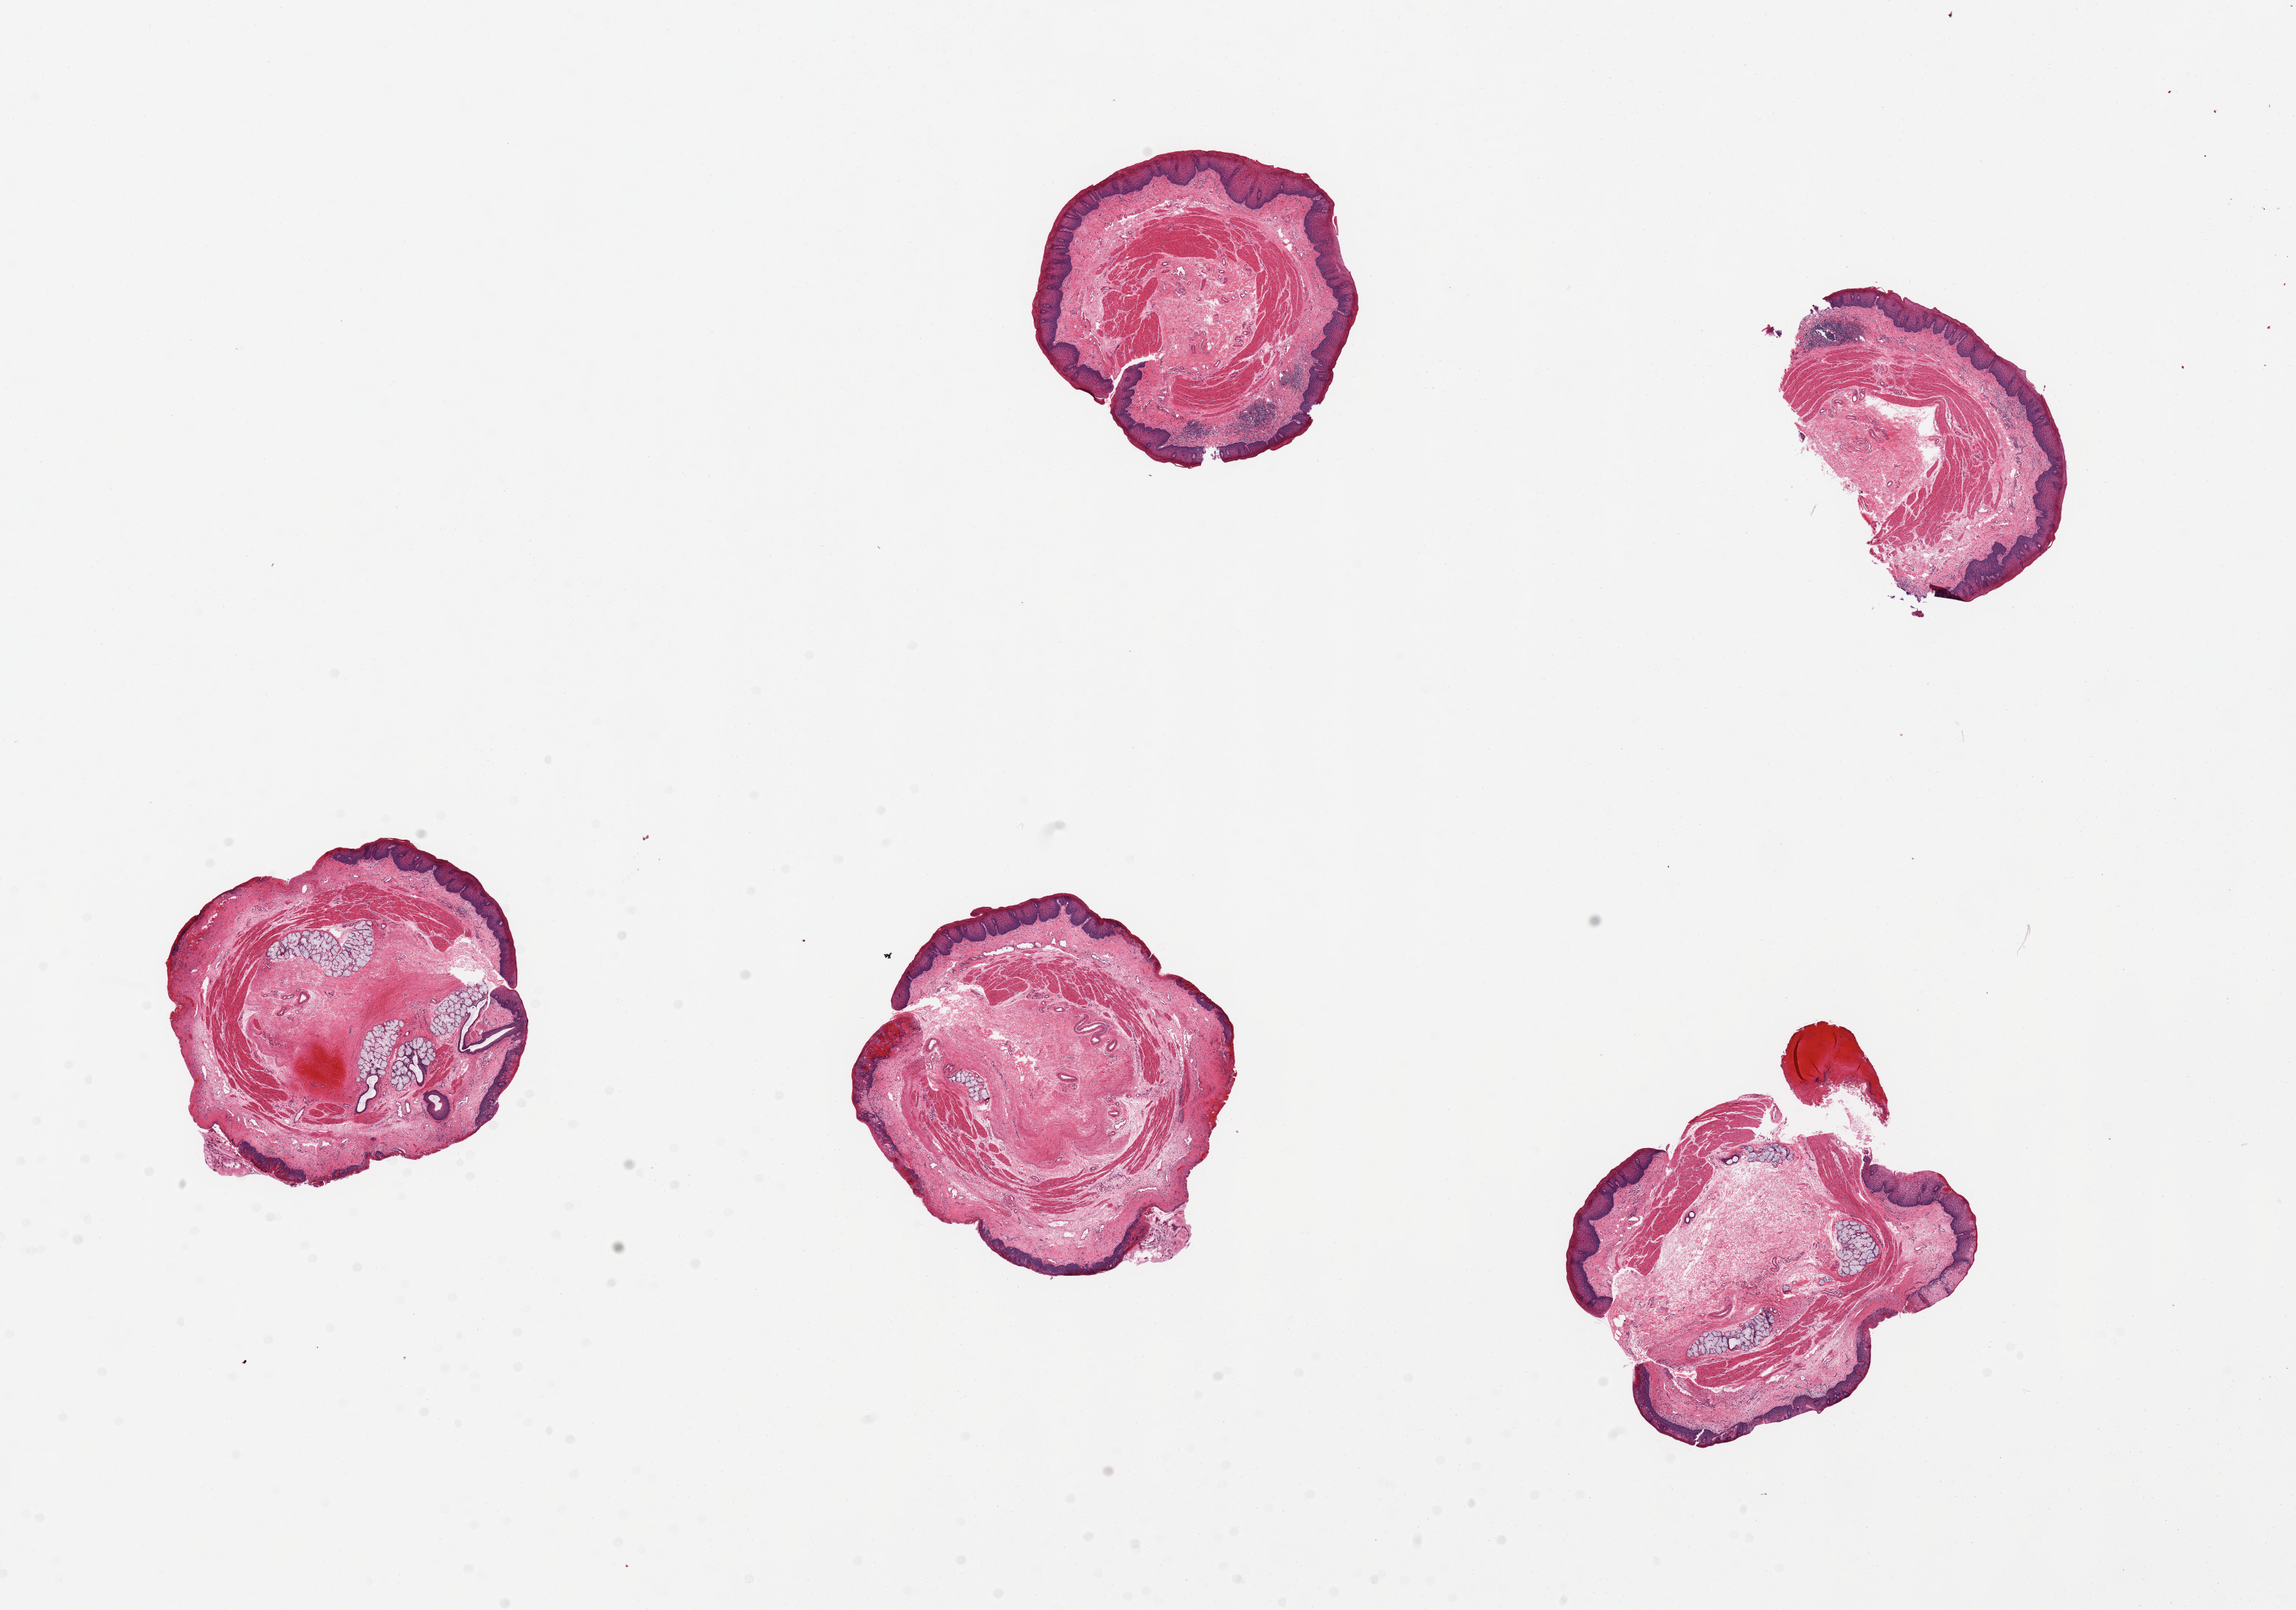
Digitized hematoxylin and eosin (H&E)-stained section, whole scanned area (about 24.6 x 17.3 mm) shown as a low-resolution overview. PAXgene-fixed, paraffin-embedded tissue. Sampled site (target tissue): esophageal mucous membrane. Donor tissue sample. Donor sex: male.
Review note (as recorded): 5 pieces; specimen is mucosa; erosions and hemorrhage.